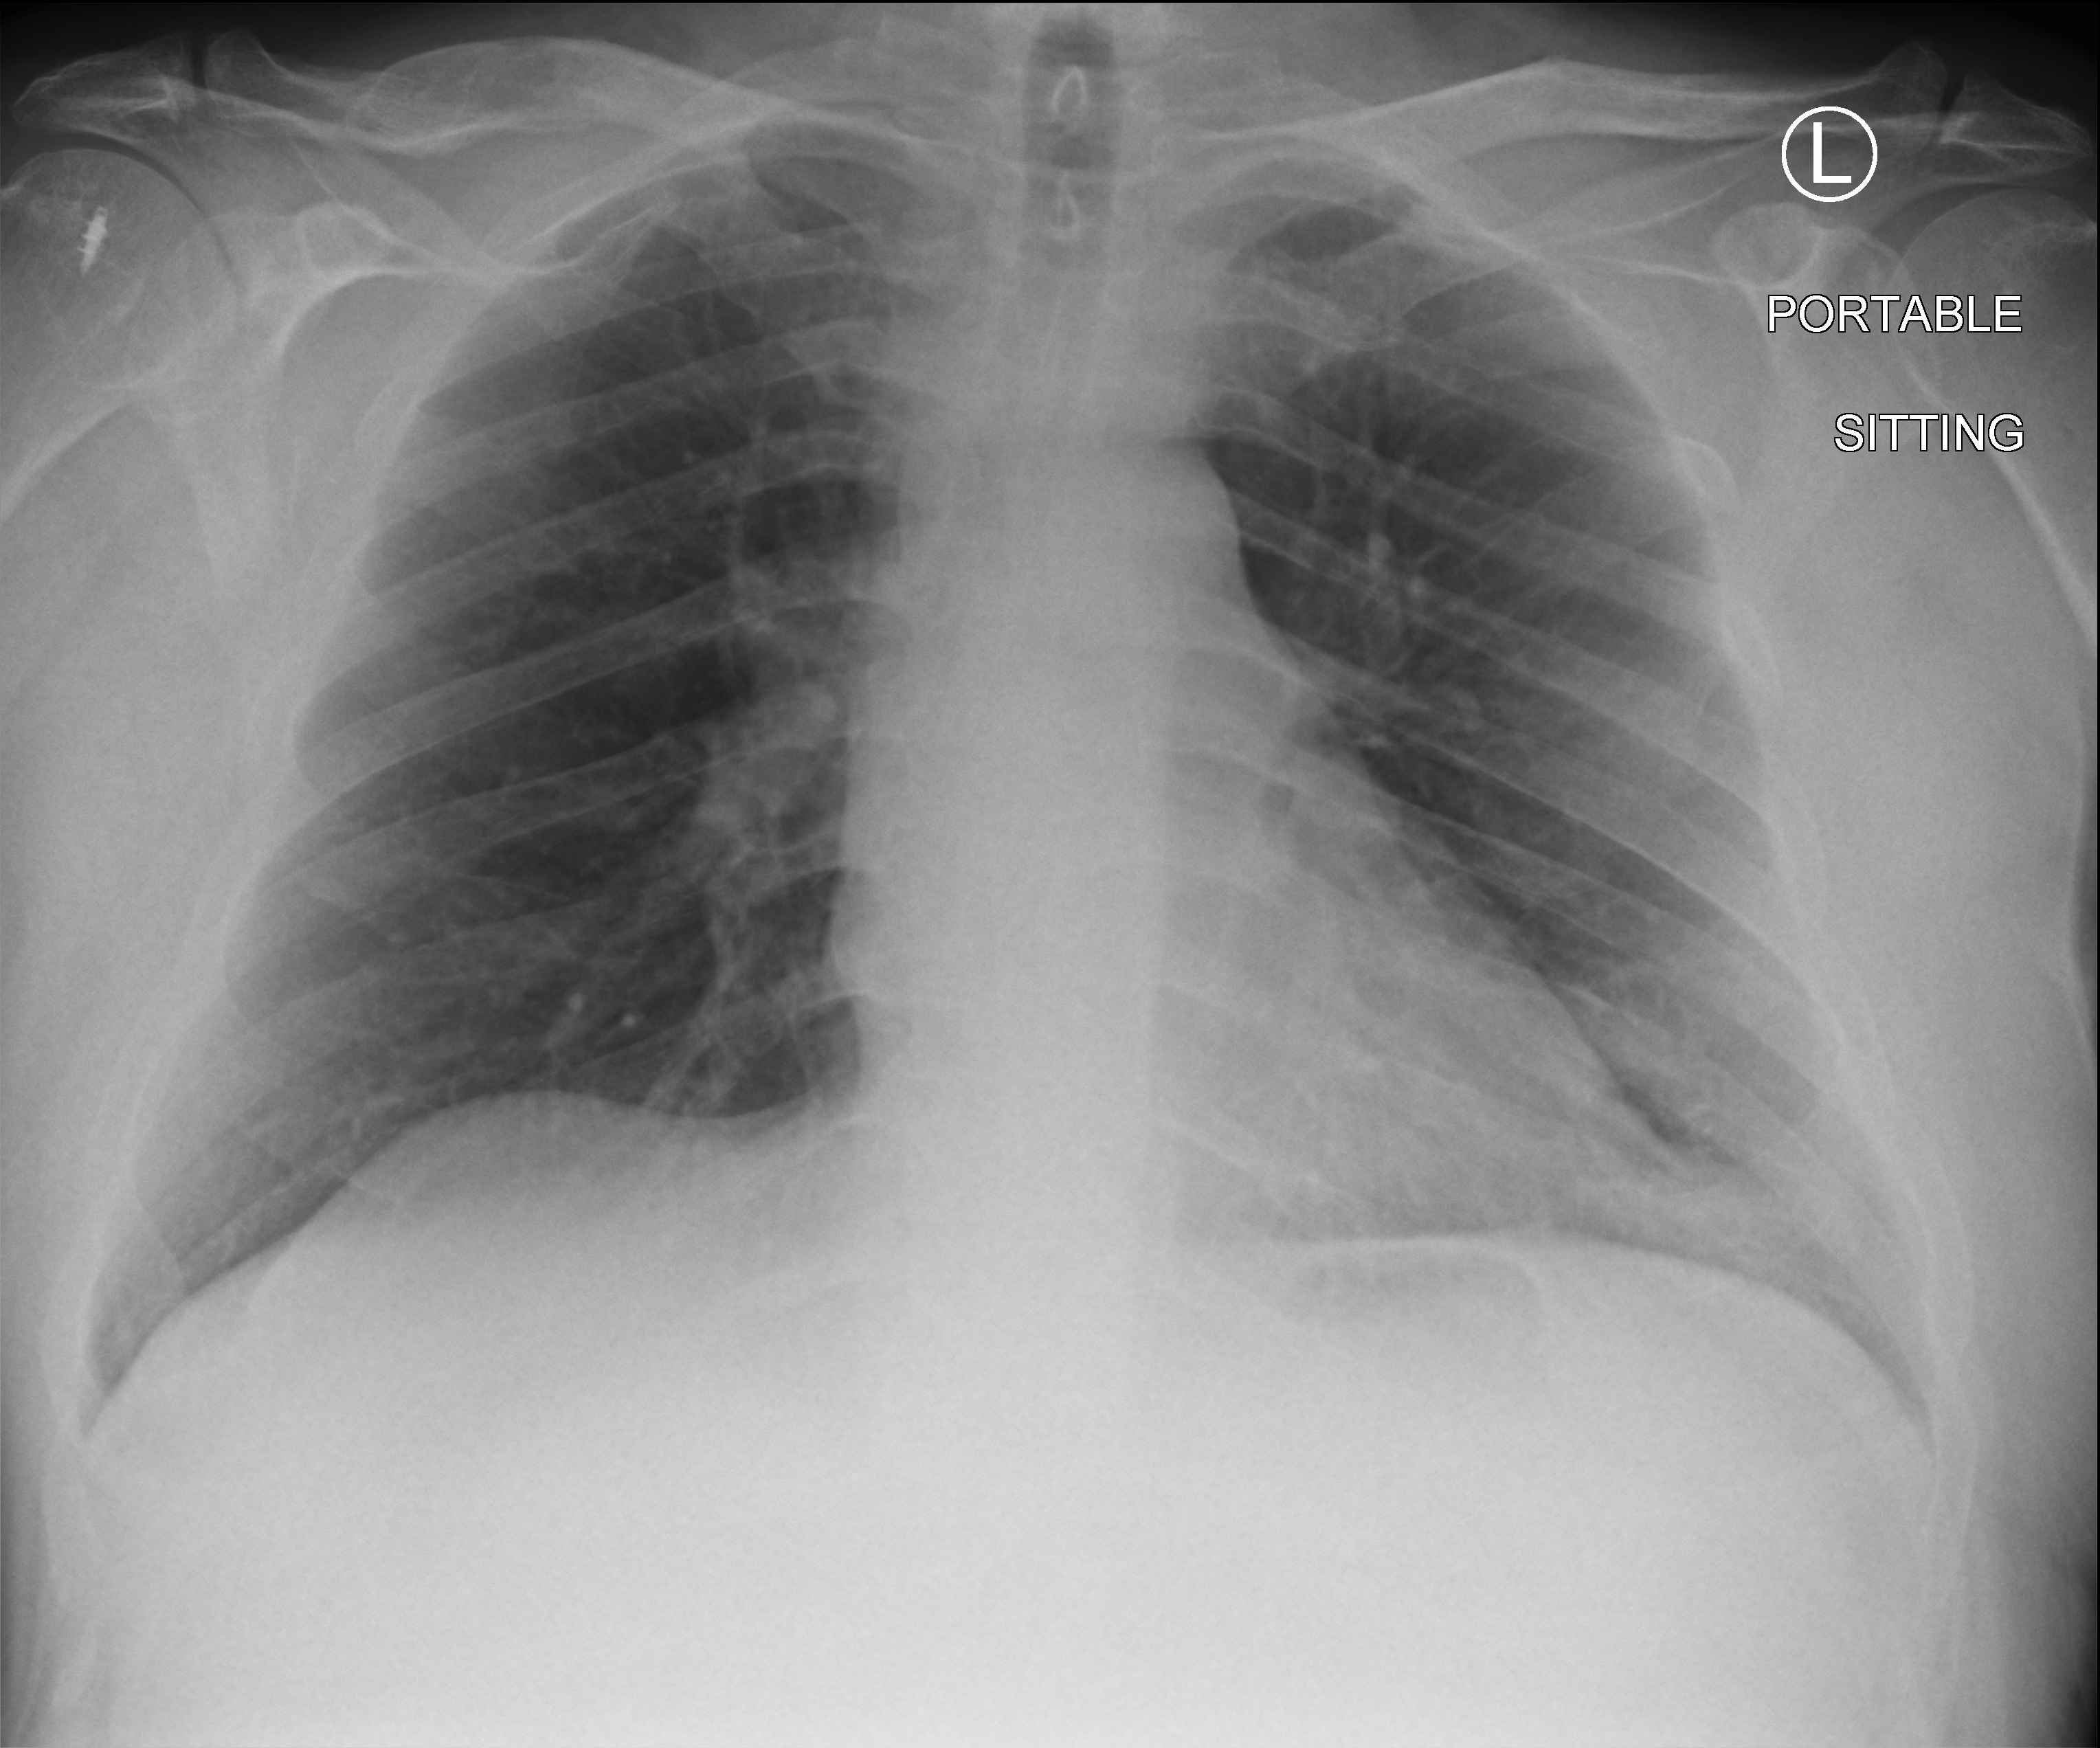
Portable chest radiograph; anteroposterior (AP) projection. Male patient hospitalised with COVID-19, age 60–74 years.
Hospital-stay facts (about this admission, not read from this image; timing relative to this image not recorded): chronic kidney disease (admission record): no.